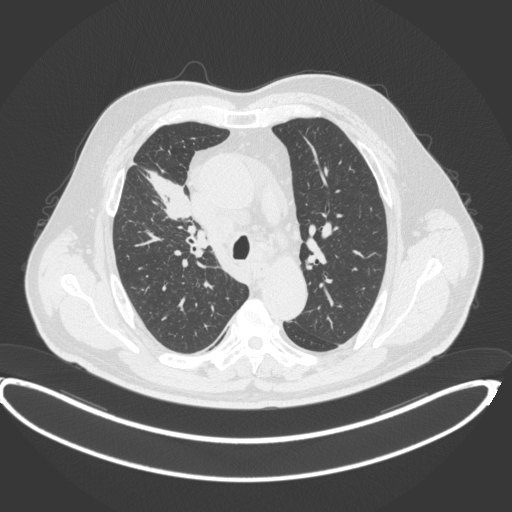
Chest CT, one axial slice. Position 284 of 395 along the scan axis. Lung window (W 1500 / L -600 HU). 1 mm slice thickness. 512 × 512 image matrix, field of view 448 × 448 mm. Male patient, age 62 years. Case-level facts recorded for this patient, not image findings: clinical TNM (as recorded): T1c N3 M1c.
Structures marked on this image (bounding box drawn by a radiologist):
- lung tumour (recorded histology: adenocarcinoma): box from (x=139, y=168) to (x=193, y=221) px